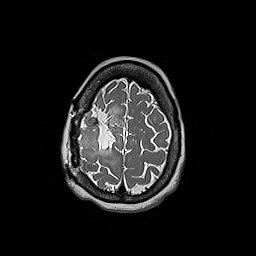
Brain MRI from a brain-tumour surgery series, one axial slice; position 49 of 192 along the scan axis; 1 mm slice thickness; 256 × 256 image matrix, field of view 250 × 250 mm. From the clinical record (not read from this slice): histopathology: Oligodendroglioma; WHO grade: 3; IDH mutation: yes.
Structures marked on this image (outlined manually by an expert reader):
- tumour: bounding box [x1, y1, x2, y2] px = [78, 111, 101, 153]